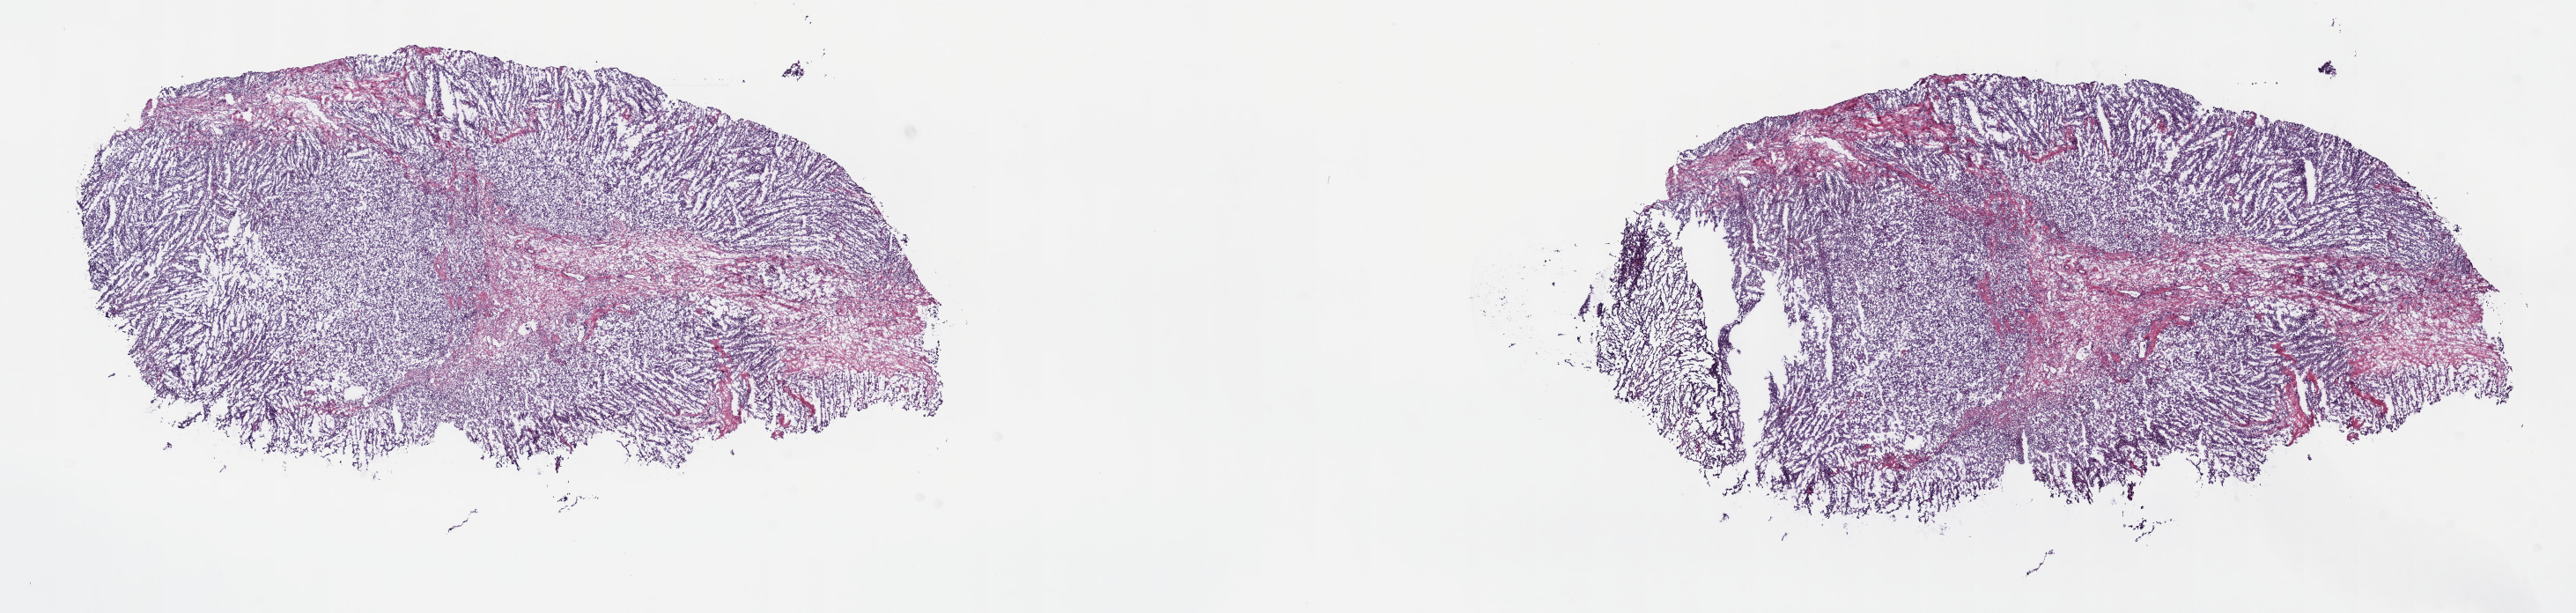
Whole-slide histology image, H&E-stained — a low-resolution overview of the entire scanned area, about 23.7 x 5.6 mm (acquisition: 40x scan). Frozen section from the top of the tissue portion. Primary tumour sample from the testis. Male patient; age at initial diagnosis 38 years. Slide review estimates, as recorded: tumour cells 70%, tumour nuclei 60%, normal cells 0%, stromal cells 30%, necrosis 0%. Infiltration values recorded for this section: lymphocyte infiltration 90%, monocyte infiltration 10%, neutrophil infiltration 0%.
- TNM: T1 N0 M0
- AJCC pathologic stage: IS
- pathologic diagnosis: Seminoma, NOS